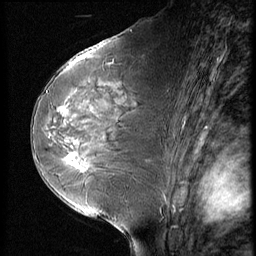
Breast MRI (dynamic contrast-enhanced), one sagittal slice. Dynamic contrast-enhanced series, image 2 of 3 at this slice position (ordered by acquisition). 1.5 T. TE 4.2 ms, TR 9 ms. 256 × 256 image matrix, field of view 180 × 180 mm. Female patient, age 58 years. From the clinical record (not read from this slice): setting: breast cancer imaged before/during neoadjuvant chemotherapy; receptor status: HR-positive, HER2-negative.
Annotated regions visible in this slice (semi-automatically segmented with operator editing):
- analysis volume of interest (the breast-tissue region the enhancement analysis was run in; not a lesion): bounding box (x1, y1, x2, y2) in pixels: (56, 146, 99, 182)
- tumour enhancement mask (voxels above the 140 % enhancement threshold inside the analysis volume of interest): (65, 153, 87, 171)